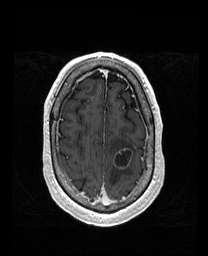
Brain MRI from a brain-tumour surgery series, one axial slice; slice 143 of 192 in the series (ordered by position); T1-weighted post-contrast; 1 mm slice thickness; 208 × 256 image matrix, field of view 211 × 260 mm. Case-level facts recorded for this patient, not image findings: histopathology: Metastatic Carcinoma from Lung Adenocarcinoma; tumour location: Left Frontal.
Structures marked on this image (expert manual segmentation):
- tumour: bounding box <113,149,132,169> (left, top, right, bottom; pixels)